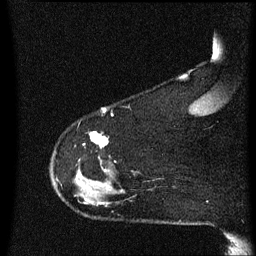
Breast MRI (dynamic contrast-enhanced), one sagittal slice; slice 52 of 60 in the series (ordered by position); dynamic contrast-enhanced series, image 2 of 3 at this slice position (ordered by acquisition); 1.5 T; TE 4.2 ms, TR 8.4 ms; 2 mm slice thickness; 256 × 256 image matrix. Patient: female, 48 years.
Annotated regions visible in this slice (semi-automatically segmented with operator editing):
- analysis volume of interest (the breast-tissue region the enhancement analysis was run in; not a lesion): box from (x=51, y=132) to (x=125, y=207) px
- tumour enhancement mask (voxels above the 70 % enhancement threshold inside the analysis volume of interest): (x=91, y=132)–(x=108, y=149)